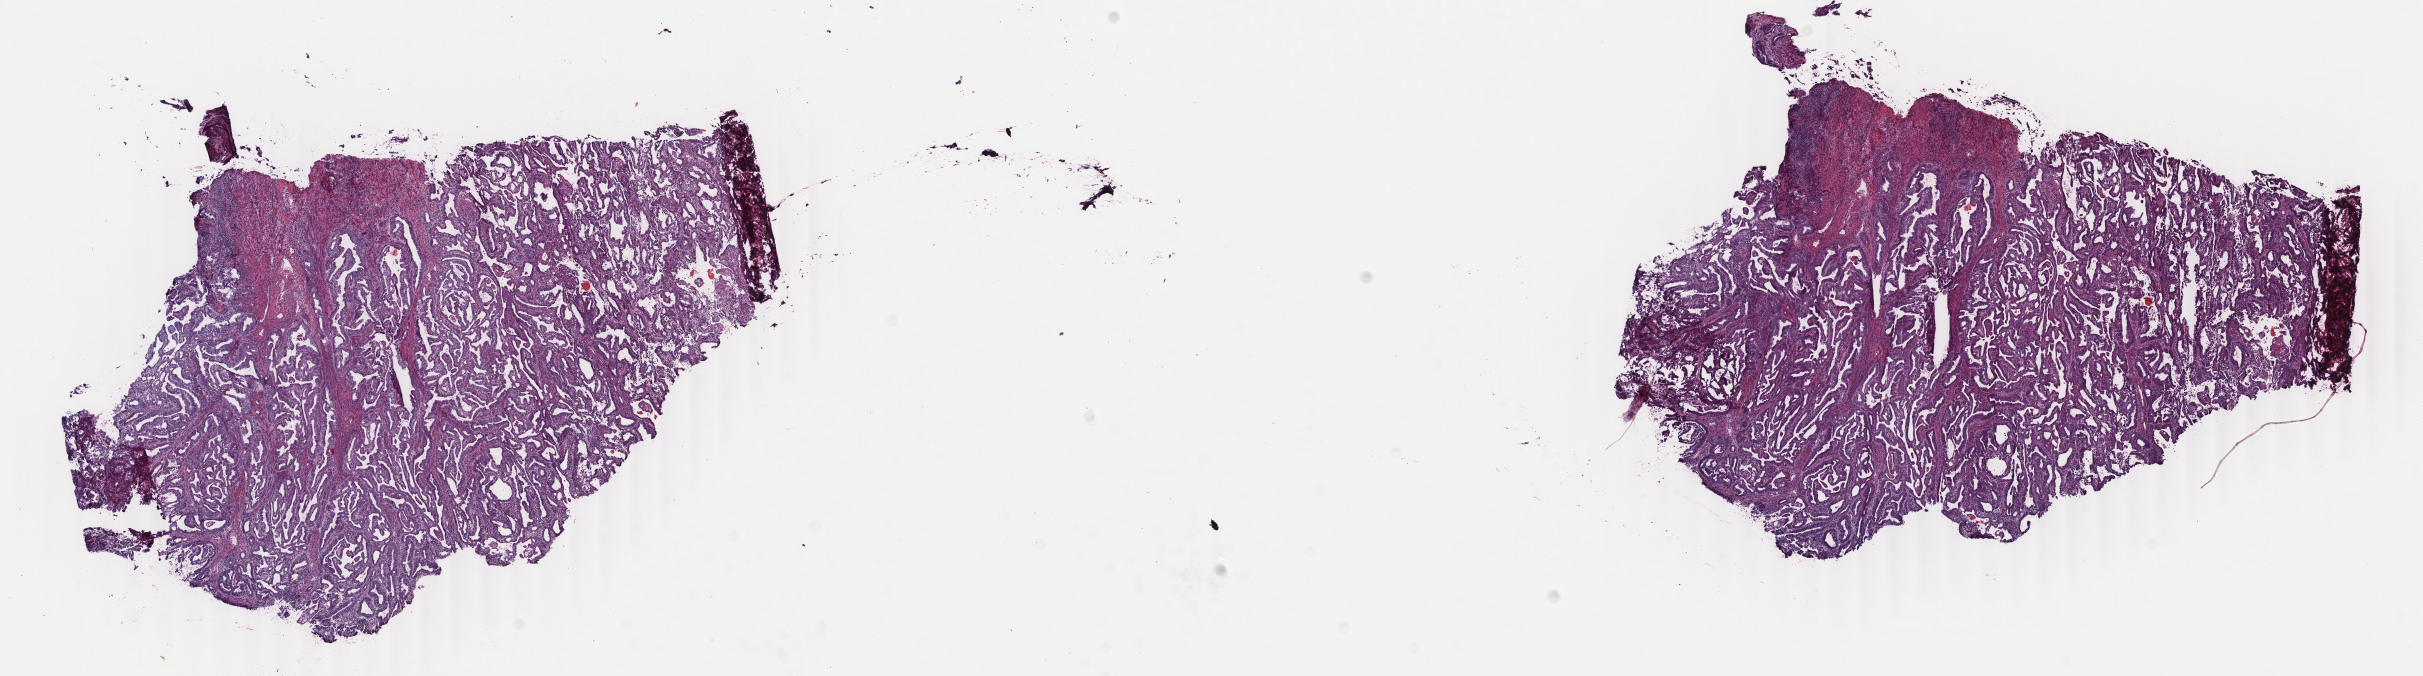
H&E-stained whole-slide image, a low-resolution overview of the entire scanned area, about 19.3 x 5.4 mm, frozen section from the top of the tissue portion, uterus, primary tumour sample. Female, age 60 years at initial diagnosis. Histologic grade: G1 (well differentiated). Slide review estimates, as recorded: tumour cells 60%, tumour nuclei 70%, normal cells 20%, stromal cells 10%, necrosis 10%. Infiltration values recorded for this section: lymphocyte infiltration 20%, monocyte infiltration 0%, neutrophil infiltration 10%.
Pathologic diagnosis: Endometrioid adenocarcinoma, NOS. FIGO stage: IA.